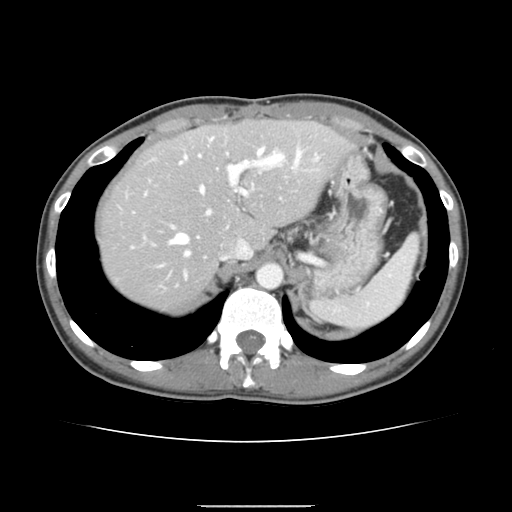
Contrast-enhanced abdominal CT, one axial slice; 120 kVp; soft-tissue window (W 400 / L 40 HU); 2.5 mm slice thickness; 512 × 512 image matrix, field of view 324 × 324 mm. Female patient, age 32 years. From the clinical record (not read from this slice): diagnosis: colorectal cancer liver metastases, imaged before liver resection; multiple liver metastases: yes; largest metastasis: 0.7 cm; disease in both lobes: no.
Structures marked on this image (manually delineated by an expert):
- hepatic veins: box from (x=157, y=150) to (x=297, y=279) px
- liver: (x=100, y=121)–(x=347, y=311)
- planned liver remnant (the part of the liver to remain after resection): (x=100, y=120)–(x=348, y=271)
- portal vein (with intrahepatic branches): (x=132, y=137)–(x=318, y=248)